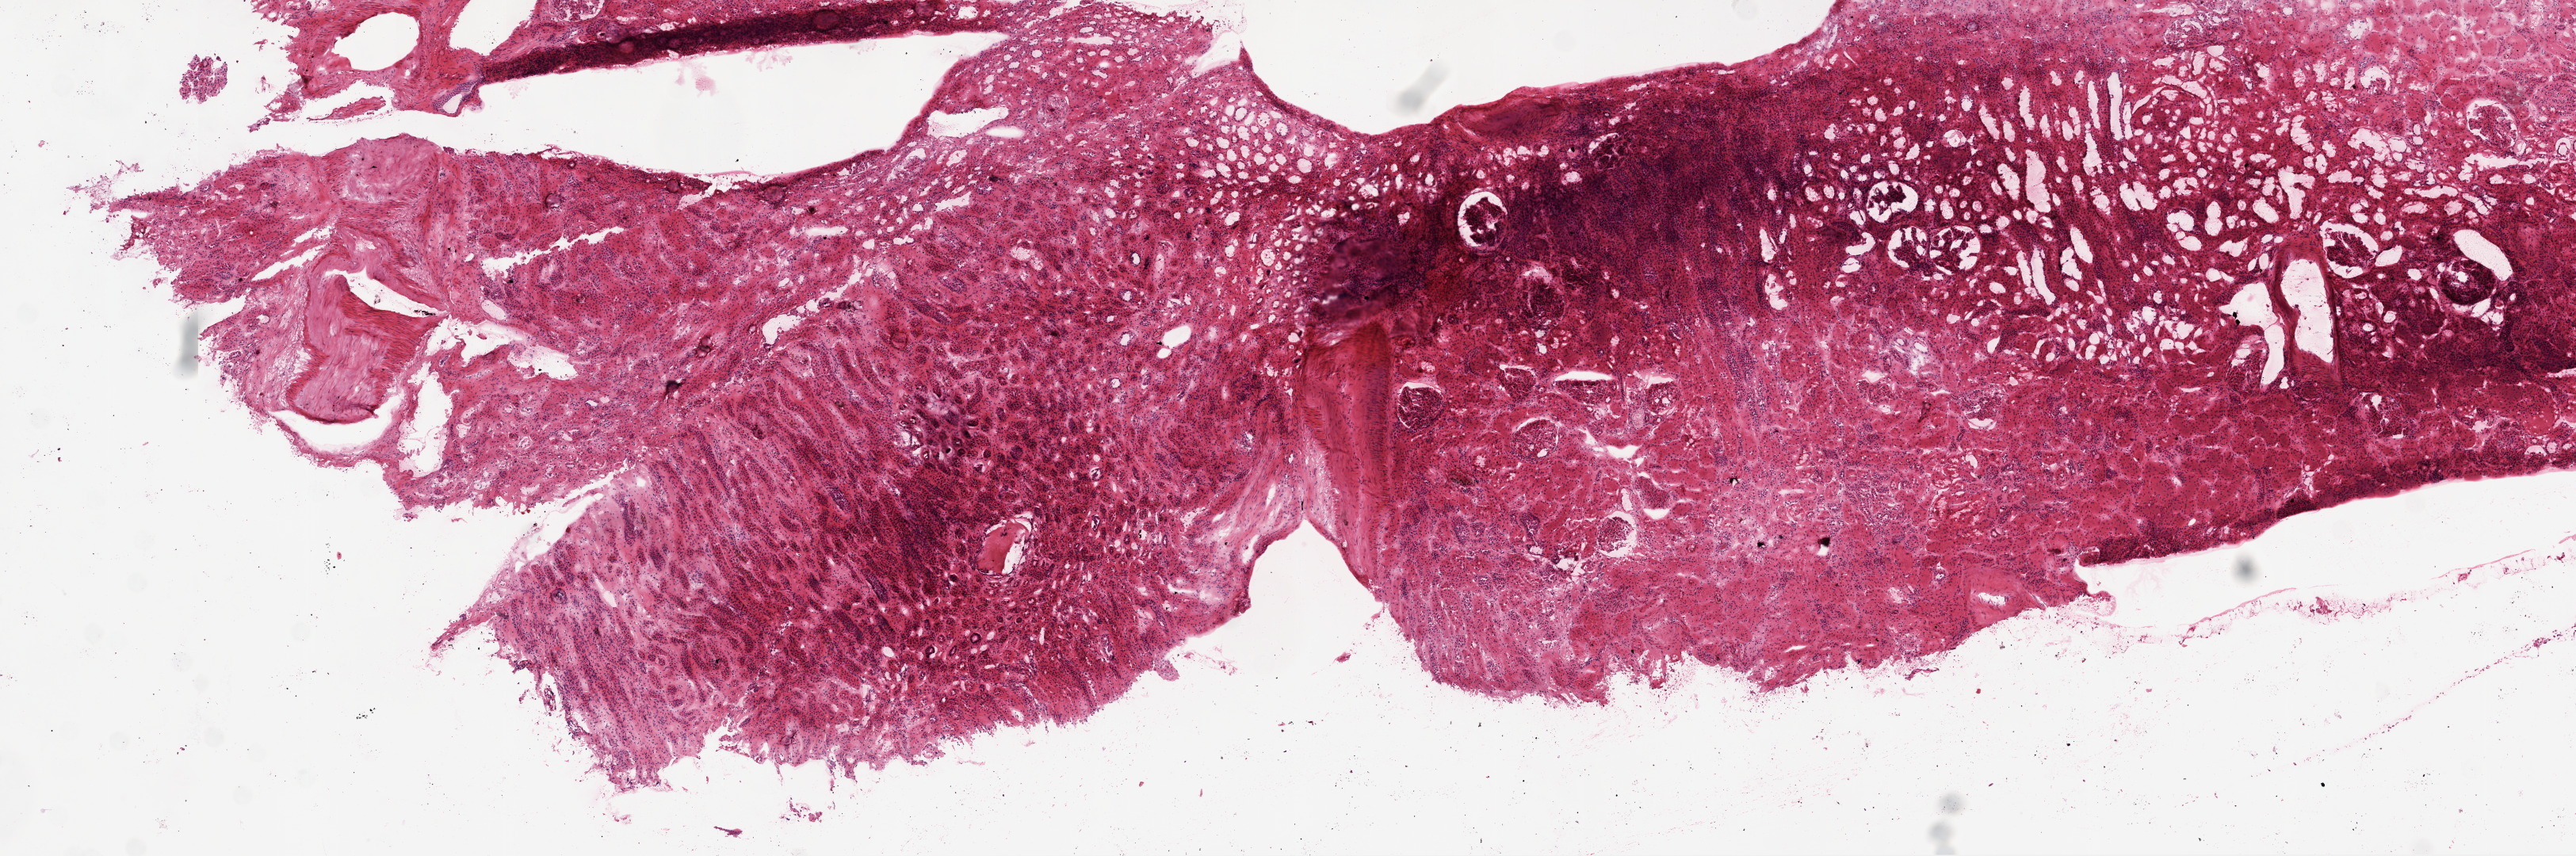
Whole-slide histology image, Hematoxylin and eosin (H&E) stained, shown as a low-resolution overview of the whole scanned area (about 13.0 x 4.3 mm, from a 20x scan), frozen section, kidney, solid tissue normal (non-tumour tissue) sample. Female patient; age at initial diagnosis 72 years.
This section: solid tissue normal sample (biorepository sample class). Patient diagnosis: Clear cell adenocarcinoma, NOS.